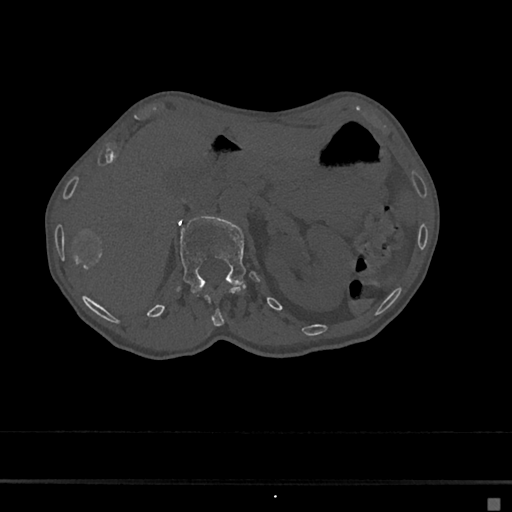
CT including the spine, one axial slice. Position 81 of 797 along the scan axis. Bone window (W 1800 / L 400 HU). 512 × 512 image matrix. Female patient, age 68 years. Case-level facts recorded for this patient, not image findings: primary cancer: renal.
Outlined on this slice (semi-automatic segmentation, software-assisted and operator-edited):
- L1 vertebra: box from (x=180, y=216) to (x=259, y=293) px
- T12 vertebra: (x=196, y=287)–(x=242, y=327)